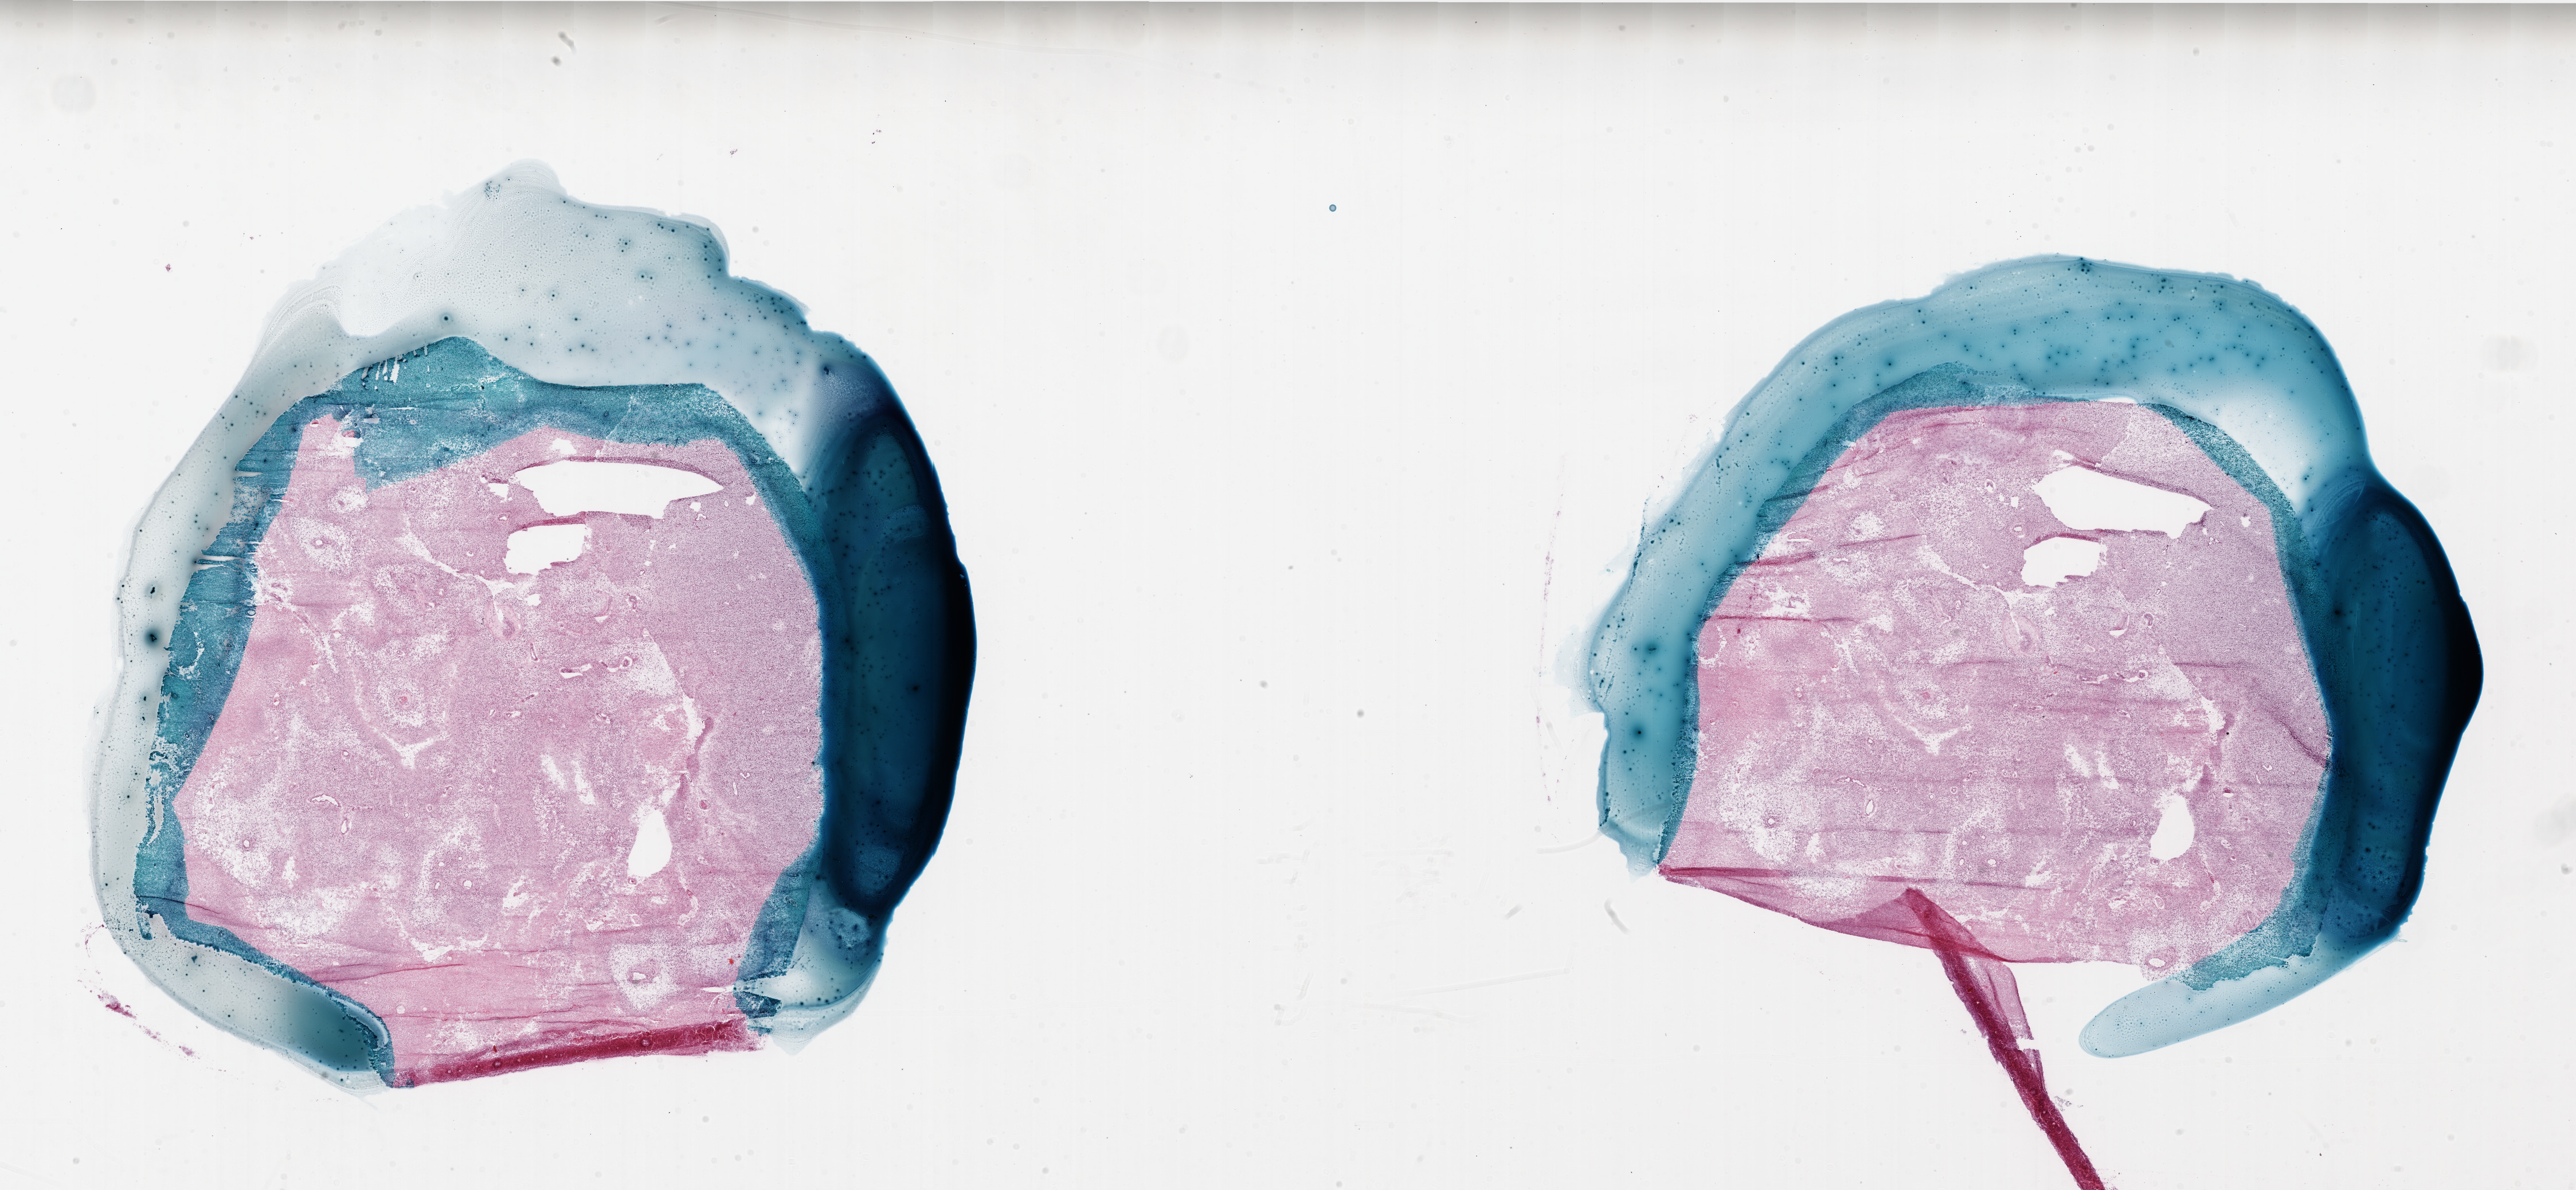
Digitized H&E-stained tissue section (whole slide), low-resolution overview of the scanned area, about 36.0 x 16.6 mm (from a 20x scan); frozen section; sample: primary tumour, brain. Female patient; age at initial diagnosis 84 years. Composition of this section per pathologist review: tumour cells 80%, tumour nuclei 100%, normal cells 0%, stromal cells 0%, necrosis 20%.
- pathologic diagnosis: Glioblastoma